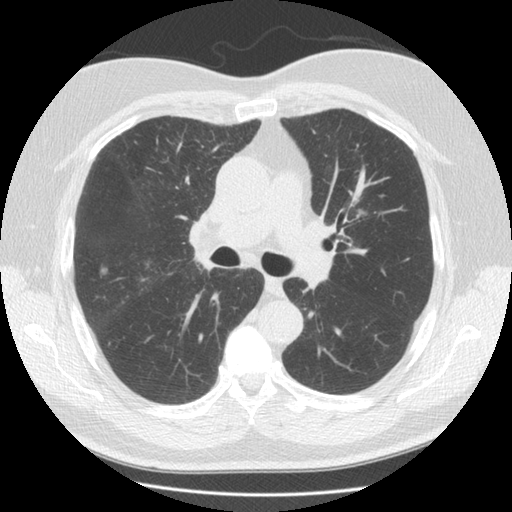
Axial slice from a low-dose chest CT screening exam. Third annual screen. Lung window (W 1500 / L -600 HU). Standard (soft-tissue) reconstruction kernel (STANDARD). Slice 60 of 146 in the series. 512 × 512 image matrix. Male participant, aged 65 years at enrolment. Former smoker at enrolment.
Expert reader's lesion annotation, bounding box [x1, y1, x2, y2] px = [89, 258, 116, 290]. The exam's reader record, not a measurement of the box and not confirmed to be the same lesion: non-calcified nodule or mass ≥4 mm, right upper lobe, 12 × 12 mm, smooth margins, soft tissue attenuation, pre-existing on the prior screen: yes; interval growth: yes. Official screen result: positive, other. Lung cancer was diagnosed 54 days after this screen: adenocarcinoma, NOS, right upper lobe, poorly differentiated (G3), stage IA (AJCC 6th edition), 17 mm at pathology.